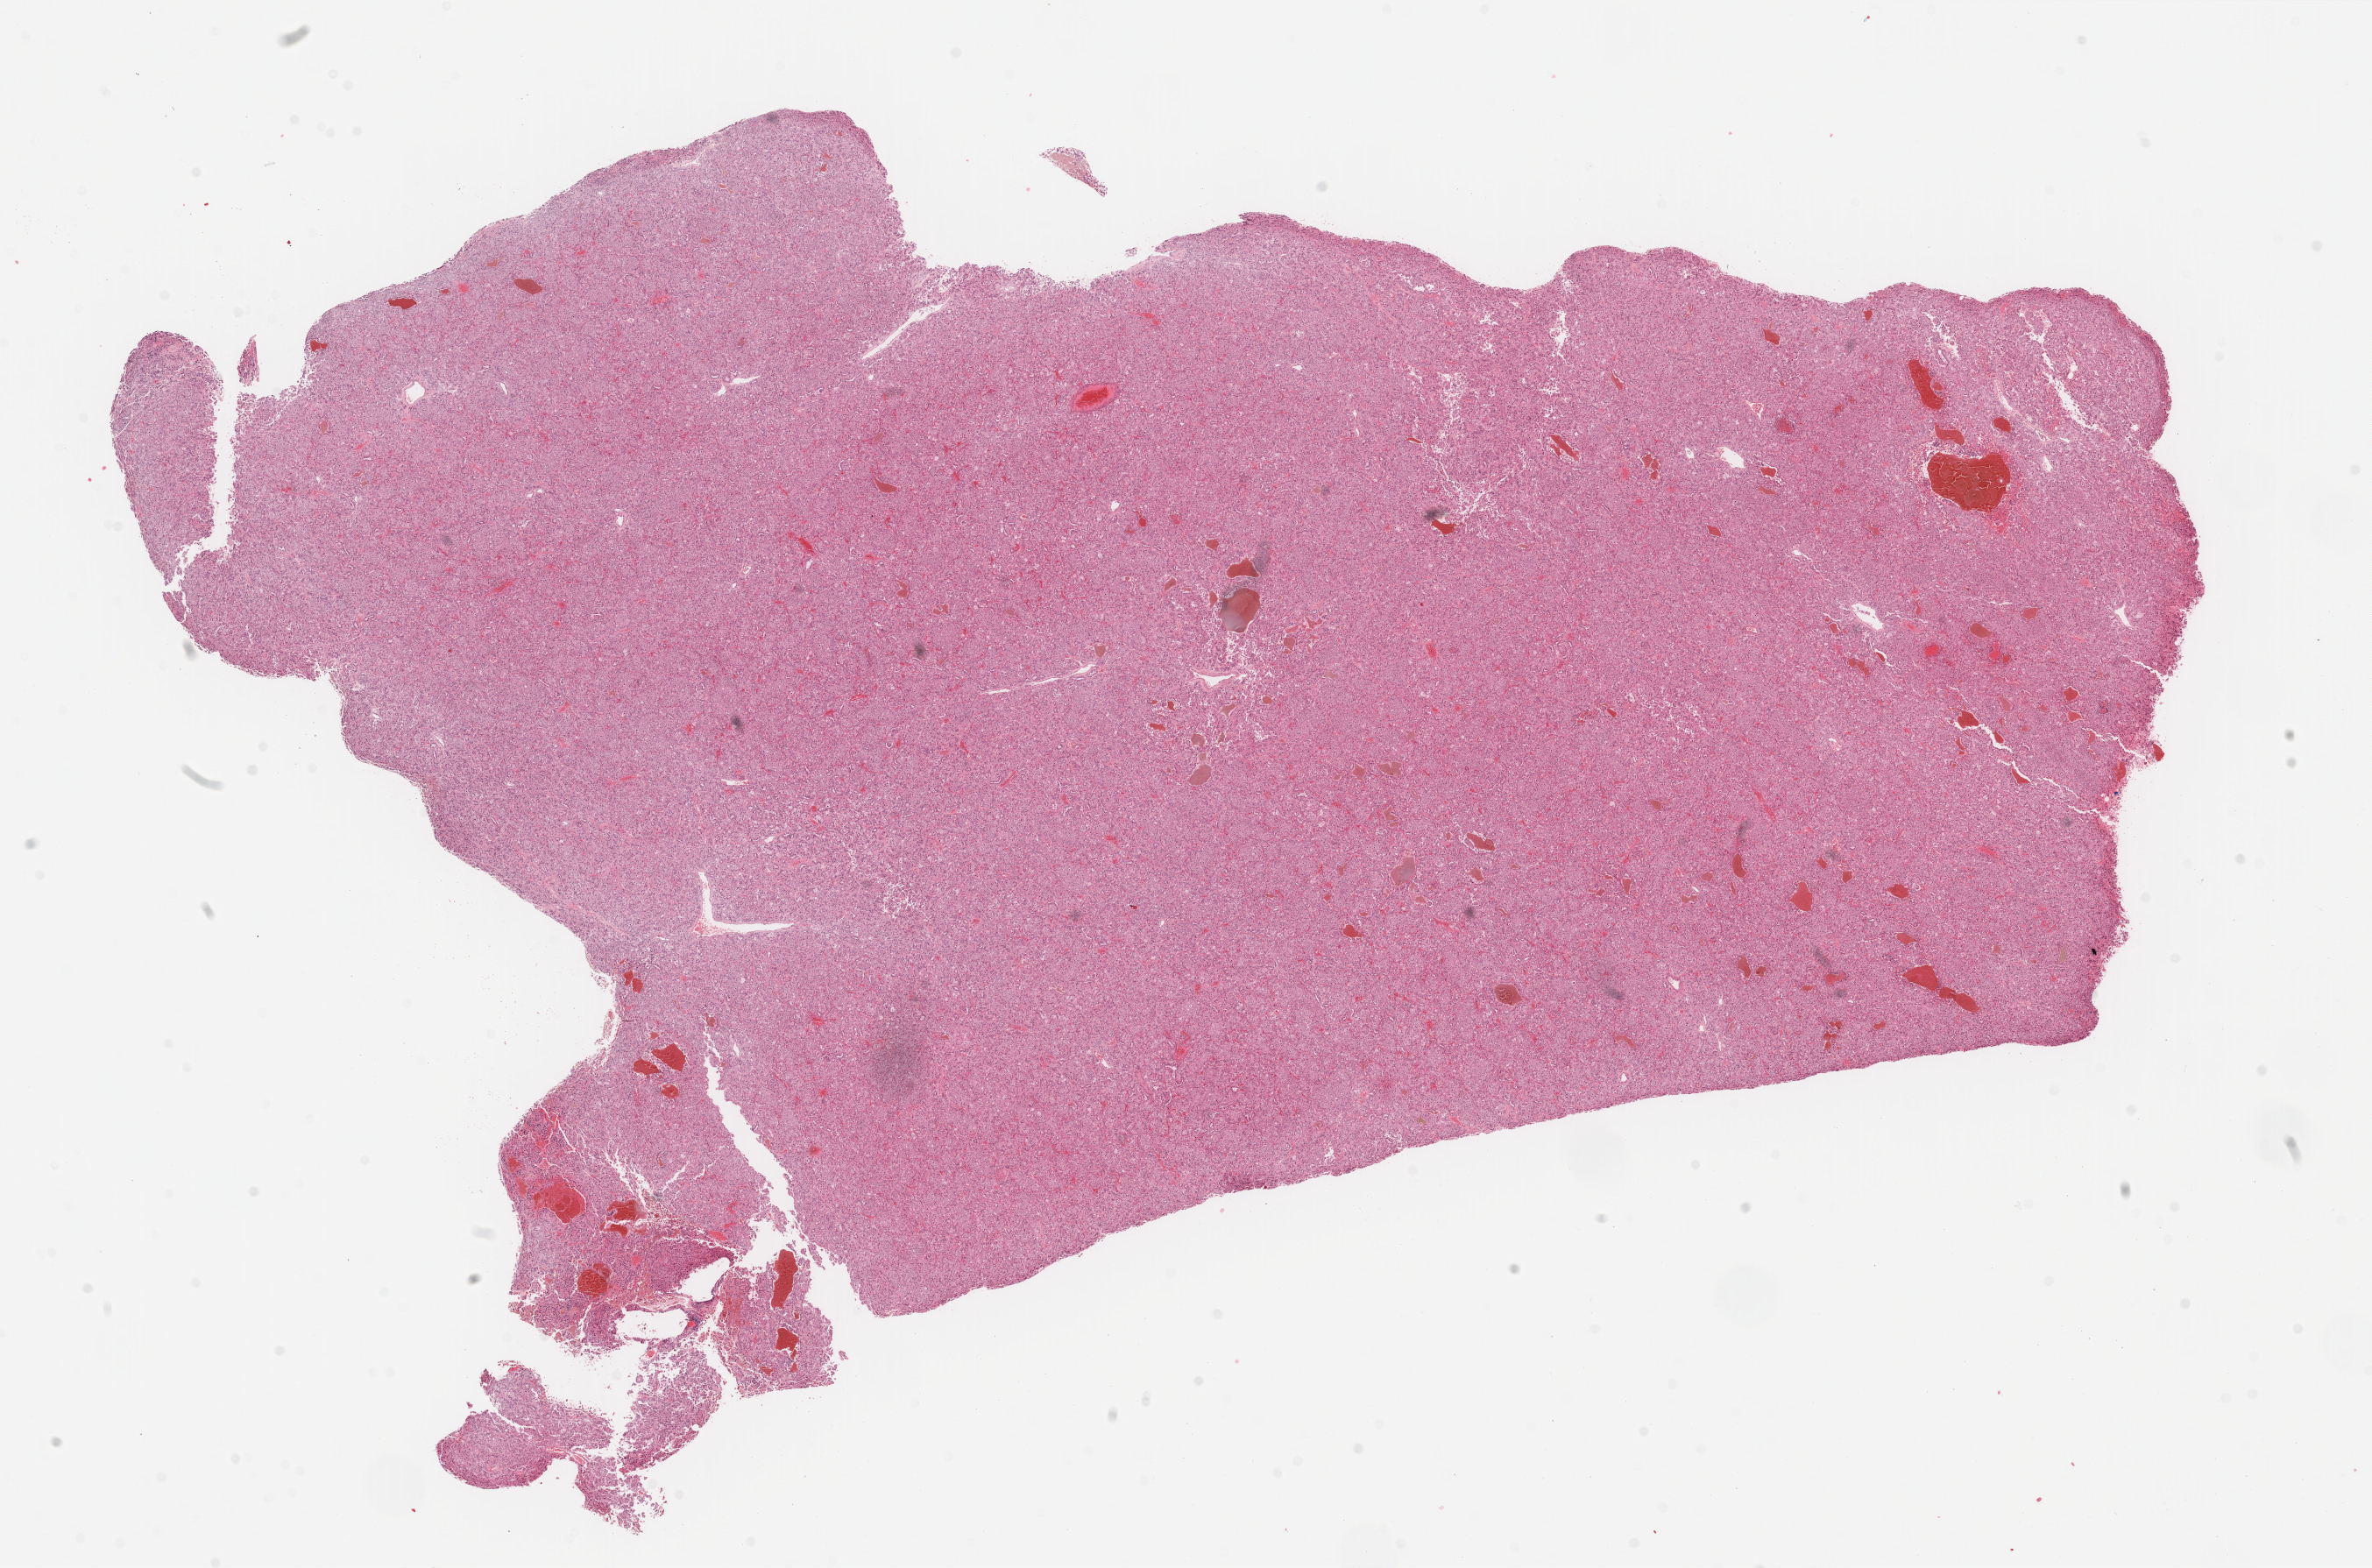
Hematoxylin and eosin (H&E) stained whole-slide image, a low-resolution overview of the entire scanned area, about 21.4 x 14.2 mm (acquisition: 40x scan); formalin-fixed paraffin-embedded (FFPE) diagnostic section; sample: primary tumour, kidney. Female patient; age at initial diagnosis 50 years.
Histologic diagnosis: Renal cell carcinoma, chromophobe type.